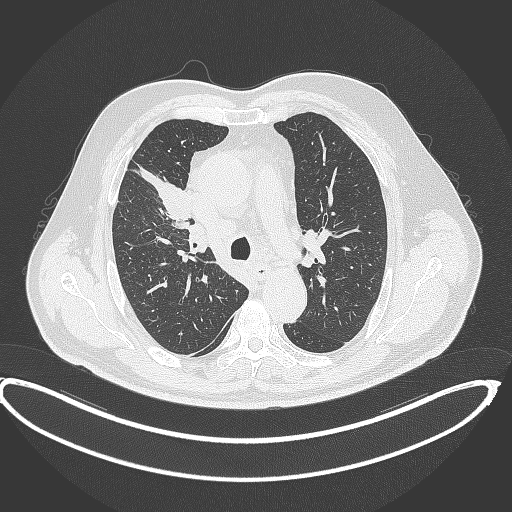
Chest CT, one axial slice; slice 278 of 390 in the series (ordered by position); 120 kVp; lung window (W 1500 / L -600 HU); 512 × 512 image matrix, field of view 448 × 448 mm. Patient: male, 62 years. From the clinical record (not read from this slice): clinical TNM (as recorded): T1c N3 M1c.
Outlined on this slice (bounding box drawn by a radiologist):
- lung tumour (recorded histology: adenocarcinoma): bounding box (x1, y1, x2, y2) in pixels: (137, 164, 194, 223)